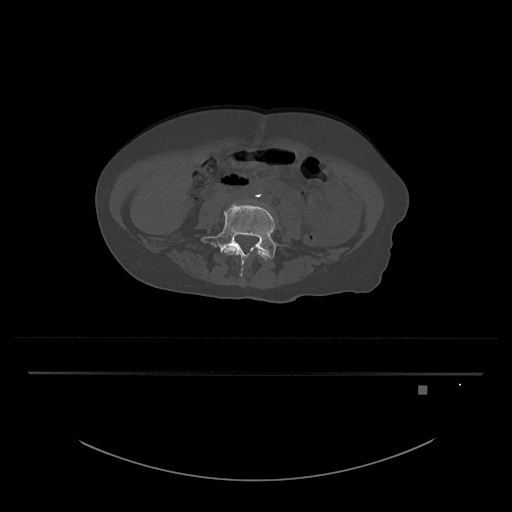
CT including the spine, one axial slice. Position 321 of 797 along the scan axis. Reconstruction kernel Br40s/3. Bone window (W 1800 / L 400 HU). 512 × 512 image matrix, field of view 500 × 500 mm. Female patient, age 57 years. From the clinical record (not read from this slice): primary cancer: cervical.
Structures marked on this image (semi-automatically segmented with operator editing):
- L4 vertebra: bounding box <224,246,271,260> (left, top, right, bottom; pixels)